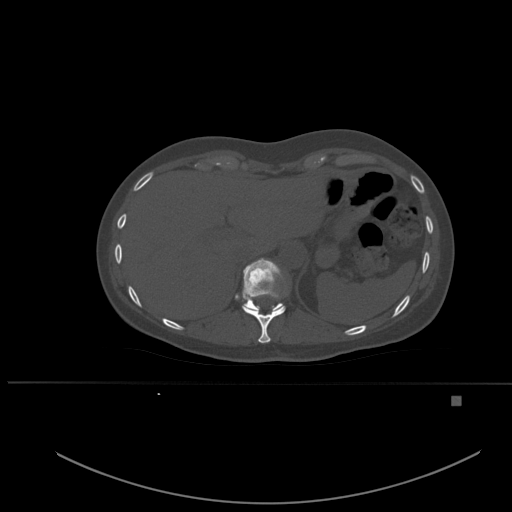
CT including the spine, one axial slice; slice 282 of 651 in the series (ordered by position); bone window (W 1800 / L 400 HU); 1.5 mm slice thickness; 512 × 512 image matrix. Female patient, age 49 years. Case-level facts recorded for this patient, not image findings: primary cancer: breast.
Structures marked on this image (semi-automatic segmentation, software-assisted and operator-edited):
- T10 vertebra: bounding box <242,290,286,343> (left, top, right, bottom; pixels)
- T11 vertebra: <242,258,283,312>